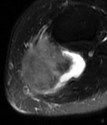
MRI of an extremity soft-tissue mass, one axial slice; slice 43 of 78 in the series (ordered by position); T2-weighted fat-saturated; MR volume resampled by the dataset authors to the PET/CT grid (not the native acquisition matrix); 3.27 mm slice thickness; 107 × 125 image matrix, field of view 104 × 122 mm. Female patient. Case-level facts recorded for this patient, not image findings: histological type: extraskeletal high grade osteogenic sarcoma; grade: high; site of the primary tumour: left calf.
Outlined on this slice (expert contour drawn on MRI and transferred to this co-registered scan by the dataset authors):
- gross tumour volume (mass): box from (x=21, y=36) to (x=86, y=96) px